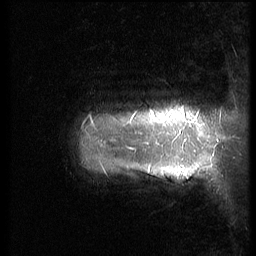
Breast MRI (dynamic contrast-enhanced), one sagittal slice. Slice 6 of 64 in the series (ordered by position). 3 images stored at this slice position (order not interpretable as contrast timing). 1.5 T. TE 4.2 ms, TR 9 ms. 2.5 mm slice thickness. 256 × 256 image matrix, field of view 180 × 180 mm. Patient: female, 39 years. Case-level facts recorded for this patient, not image findings: setting: breast cancer imaged before/during neoadjuvant chemotherapy; receptor status: HER2-positive.
Structures marked on this image (semi-automatic segmentation, software-assisted and operator-edited):
- analysis volume of interest (the breast-tissue region the enhancement analysis was run in; not a lesion): bounding box (x1, y1, x2, y2) in pixels: (63, 63, 210, 218)
- tumour enhancement mask (voxels above the 140 % enhancement threshold inside the analysis volume of interest): (89, 111, 153, 150)